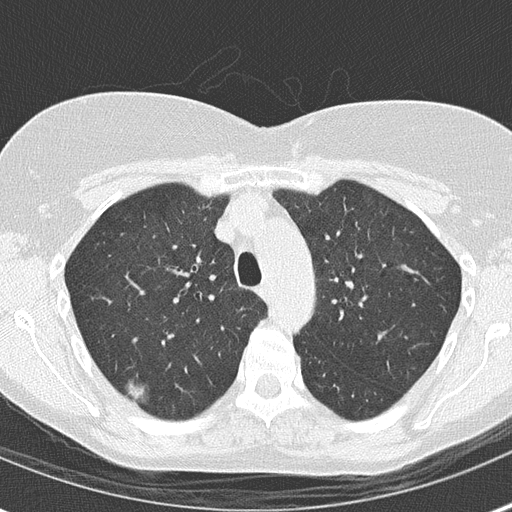
Chest CT (low-dose screening protocol), one axial image, first (baseline) screen, lung window (W 1500 / L -600 HU), 120 kVp. Female participant, aged 56 years at enrolment.
- Expert reader's lesion annotation, bounding box <110,362,161,414> (left, top, right, bottom; pixels).
- The screening reader recorded 2 non-calcified nodules or masses ≥4 mm on this exam (right upper lobe, left upper lobe); which of them this box marks is not recorded.
- Official screen result: positive, change unspecified: nodule(s) >= 4 mm or enlarging nodule(s), mass(es), or other non-specific abnormalities suspicious for lung cancer.
- Lung cancer was diagnosed 457 days after this screen (after the second annual screen): bronchiolo-alveolar adenocarcinoma, NOS, right upper lobe, well differentiated (G1), stage IA (AJCC 6th edition), 15 mm at pathology.